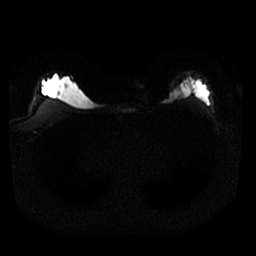
Breast MRI, one axial slice; slice 24 of 25 in the series (ordered by position); diffusion-weighted series; image 2 of 4 stored at this slice position (different b-values; order by instance number); 1.5 T; 4 mm slice thickness; 256 × 256 image matrix, field of view 320 × 320 mm. Female patient.
Outlined on this slice (manually delineated by an expert):
- tumour on diffusion-weighted imaging: bounding box [x1, y1, x2, y2] px = [174, 90, 180, 97]